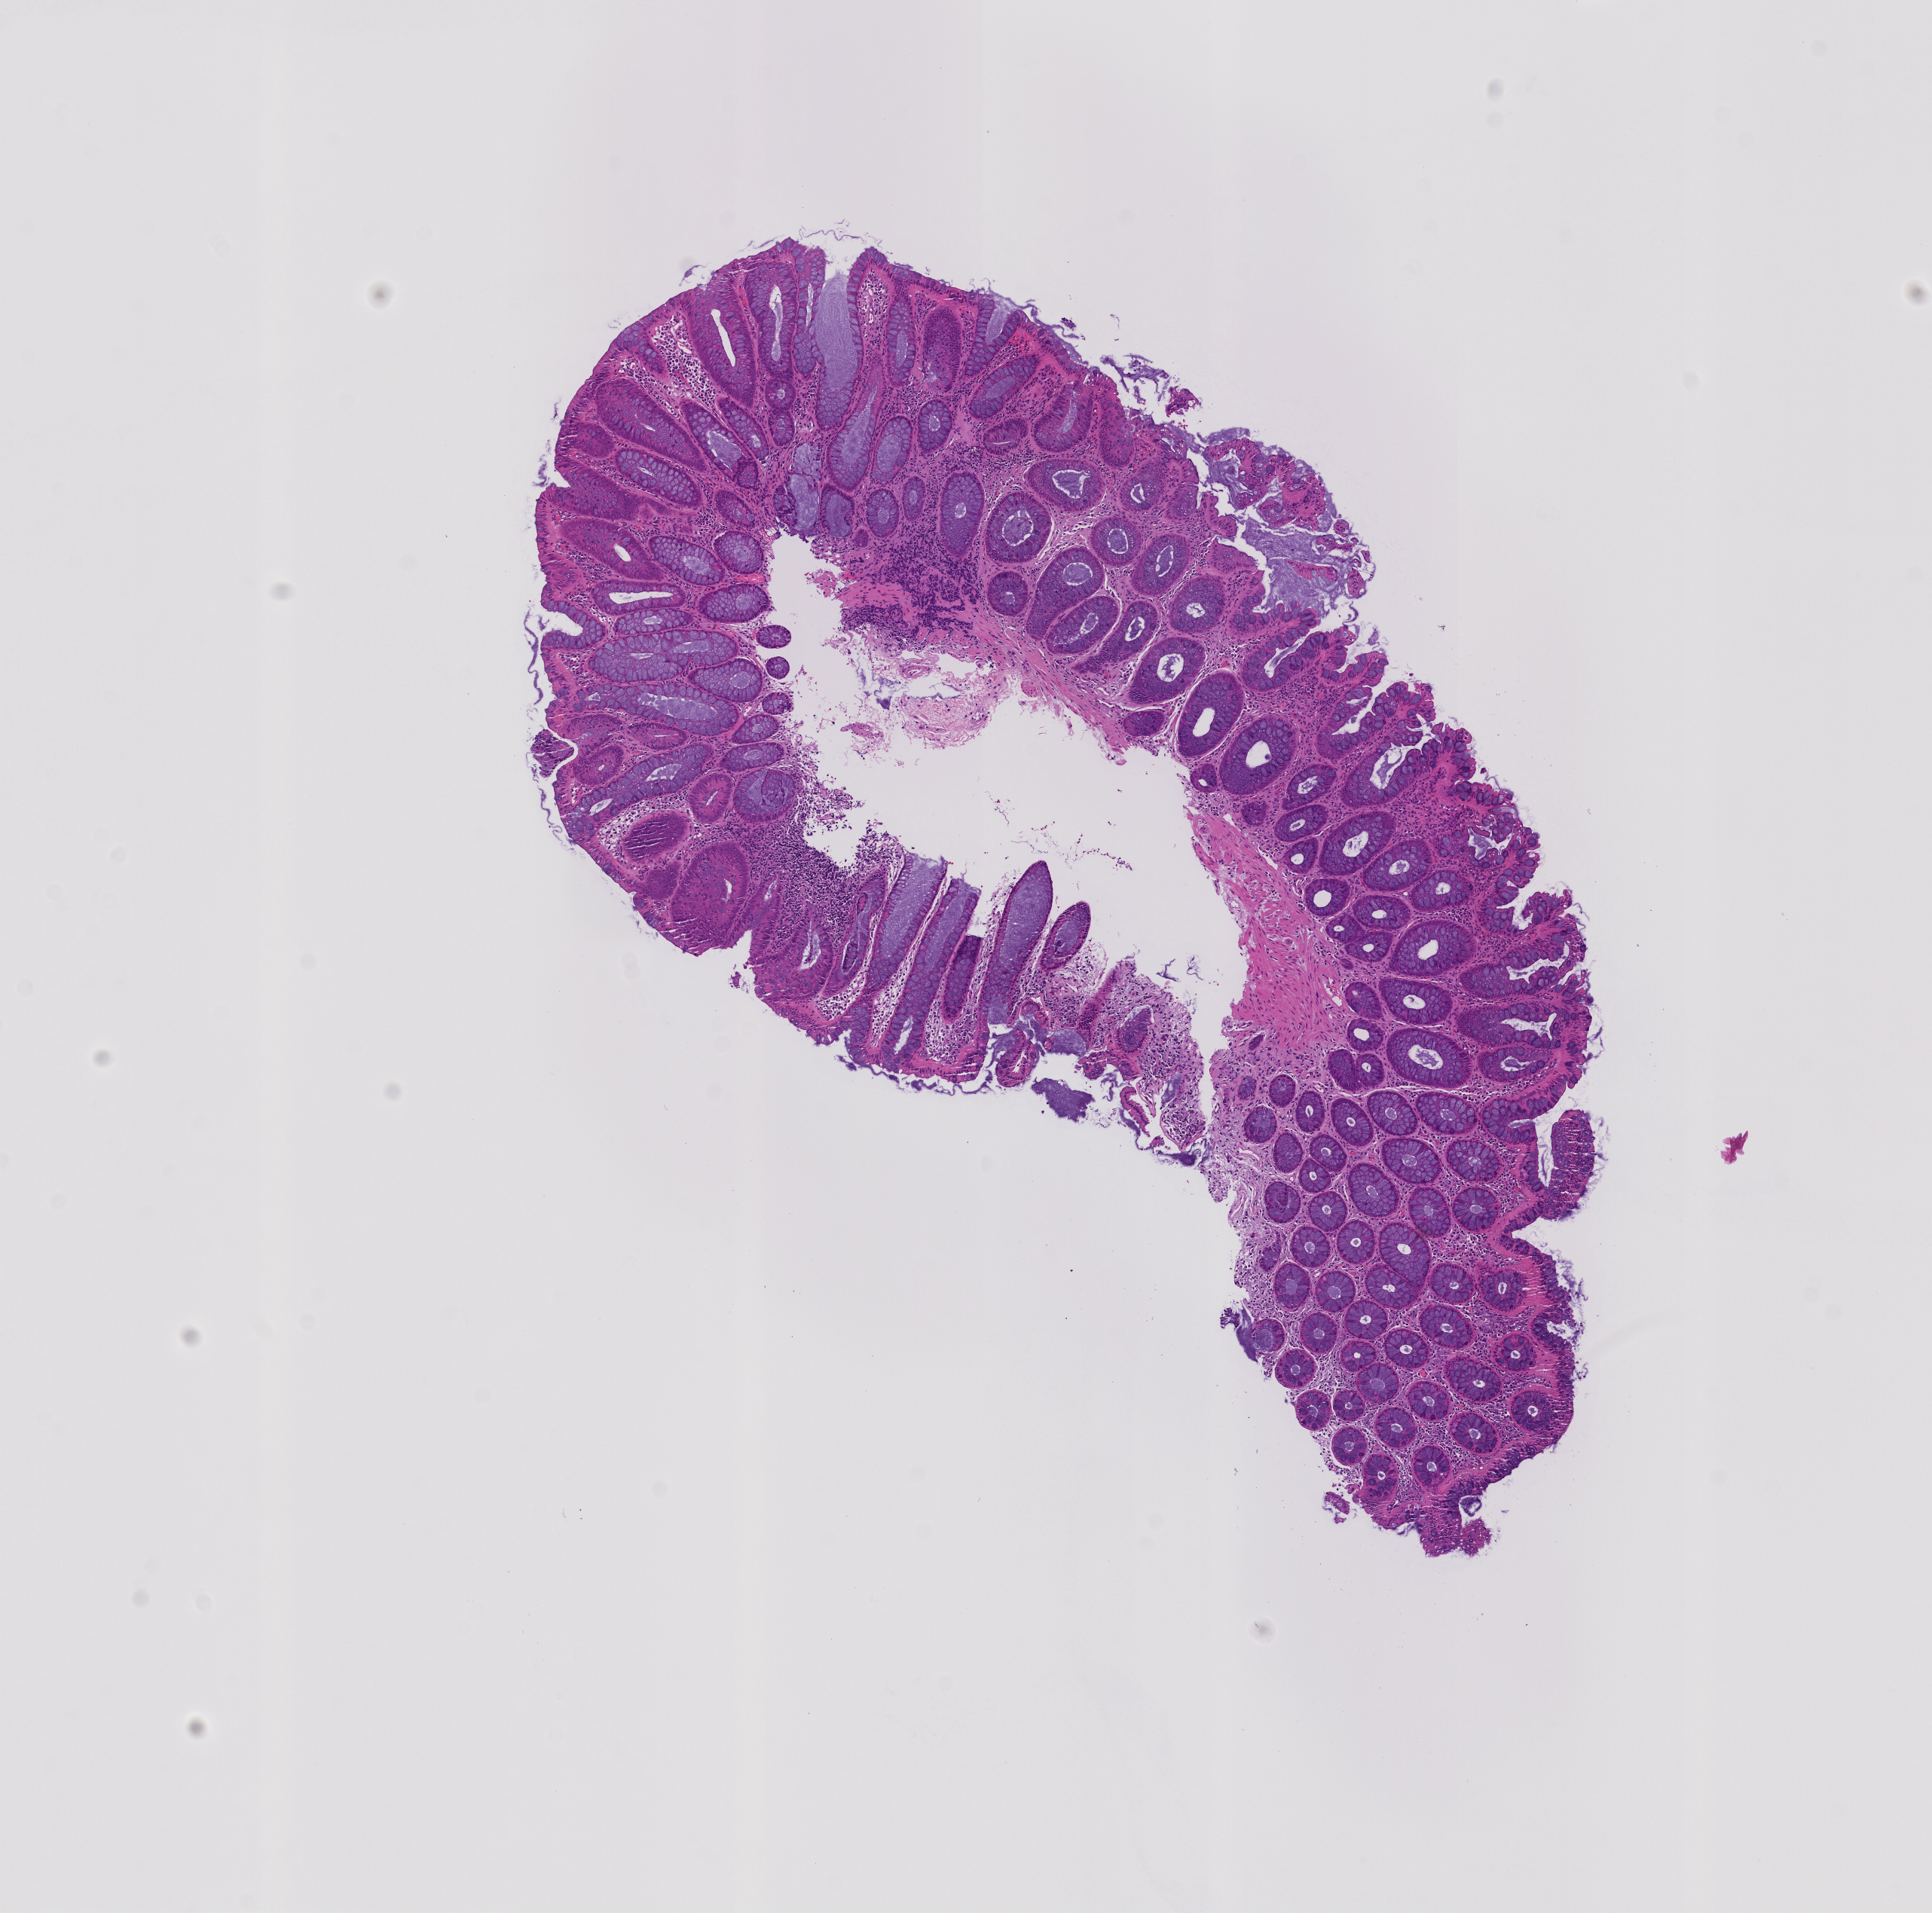
Whole-slide image, haematoxylin and eosin stain: colon biopsy, shown as a low-resolution overview of the whole scanned area (about 5.1 x 5.1 mm), formalin-fixed, paraffin-embedded (FFPE) tissue, rectum. Patient sex: male.
Lesion category (as recorded): premalignant.